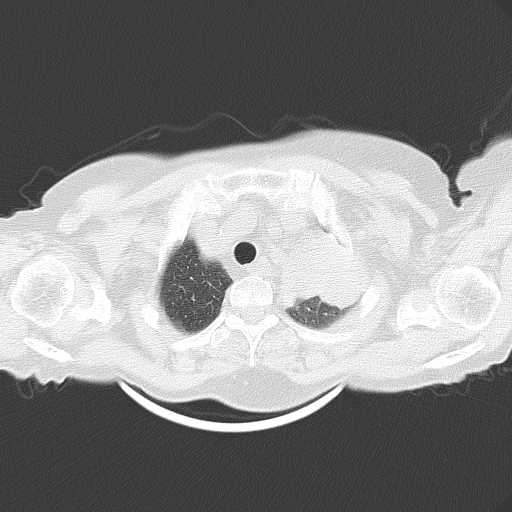
Chest CT, one axial slice. Slice 47 of 54 in the series (ordered by position). Reconstruction kernel B70f. 120 kVp. Lung window (W 1500 / L -600 HU). 5 mm slice thickness. 512 × 512 image matrix. Patient: female, 71 years. Case-level facts recorded for this patient, not image findings: clinical TNM (as recorded): T3 N3 M0.
Annotated regions visible in this slice (rectangle marked by the reading radiologist):
- lung tumour (recorded histology: adenocarcinoma): bounding box [x1, y1, x2, y2] px = [267, 215, 371, 318]